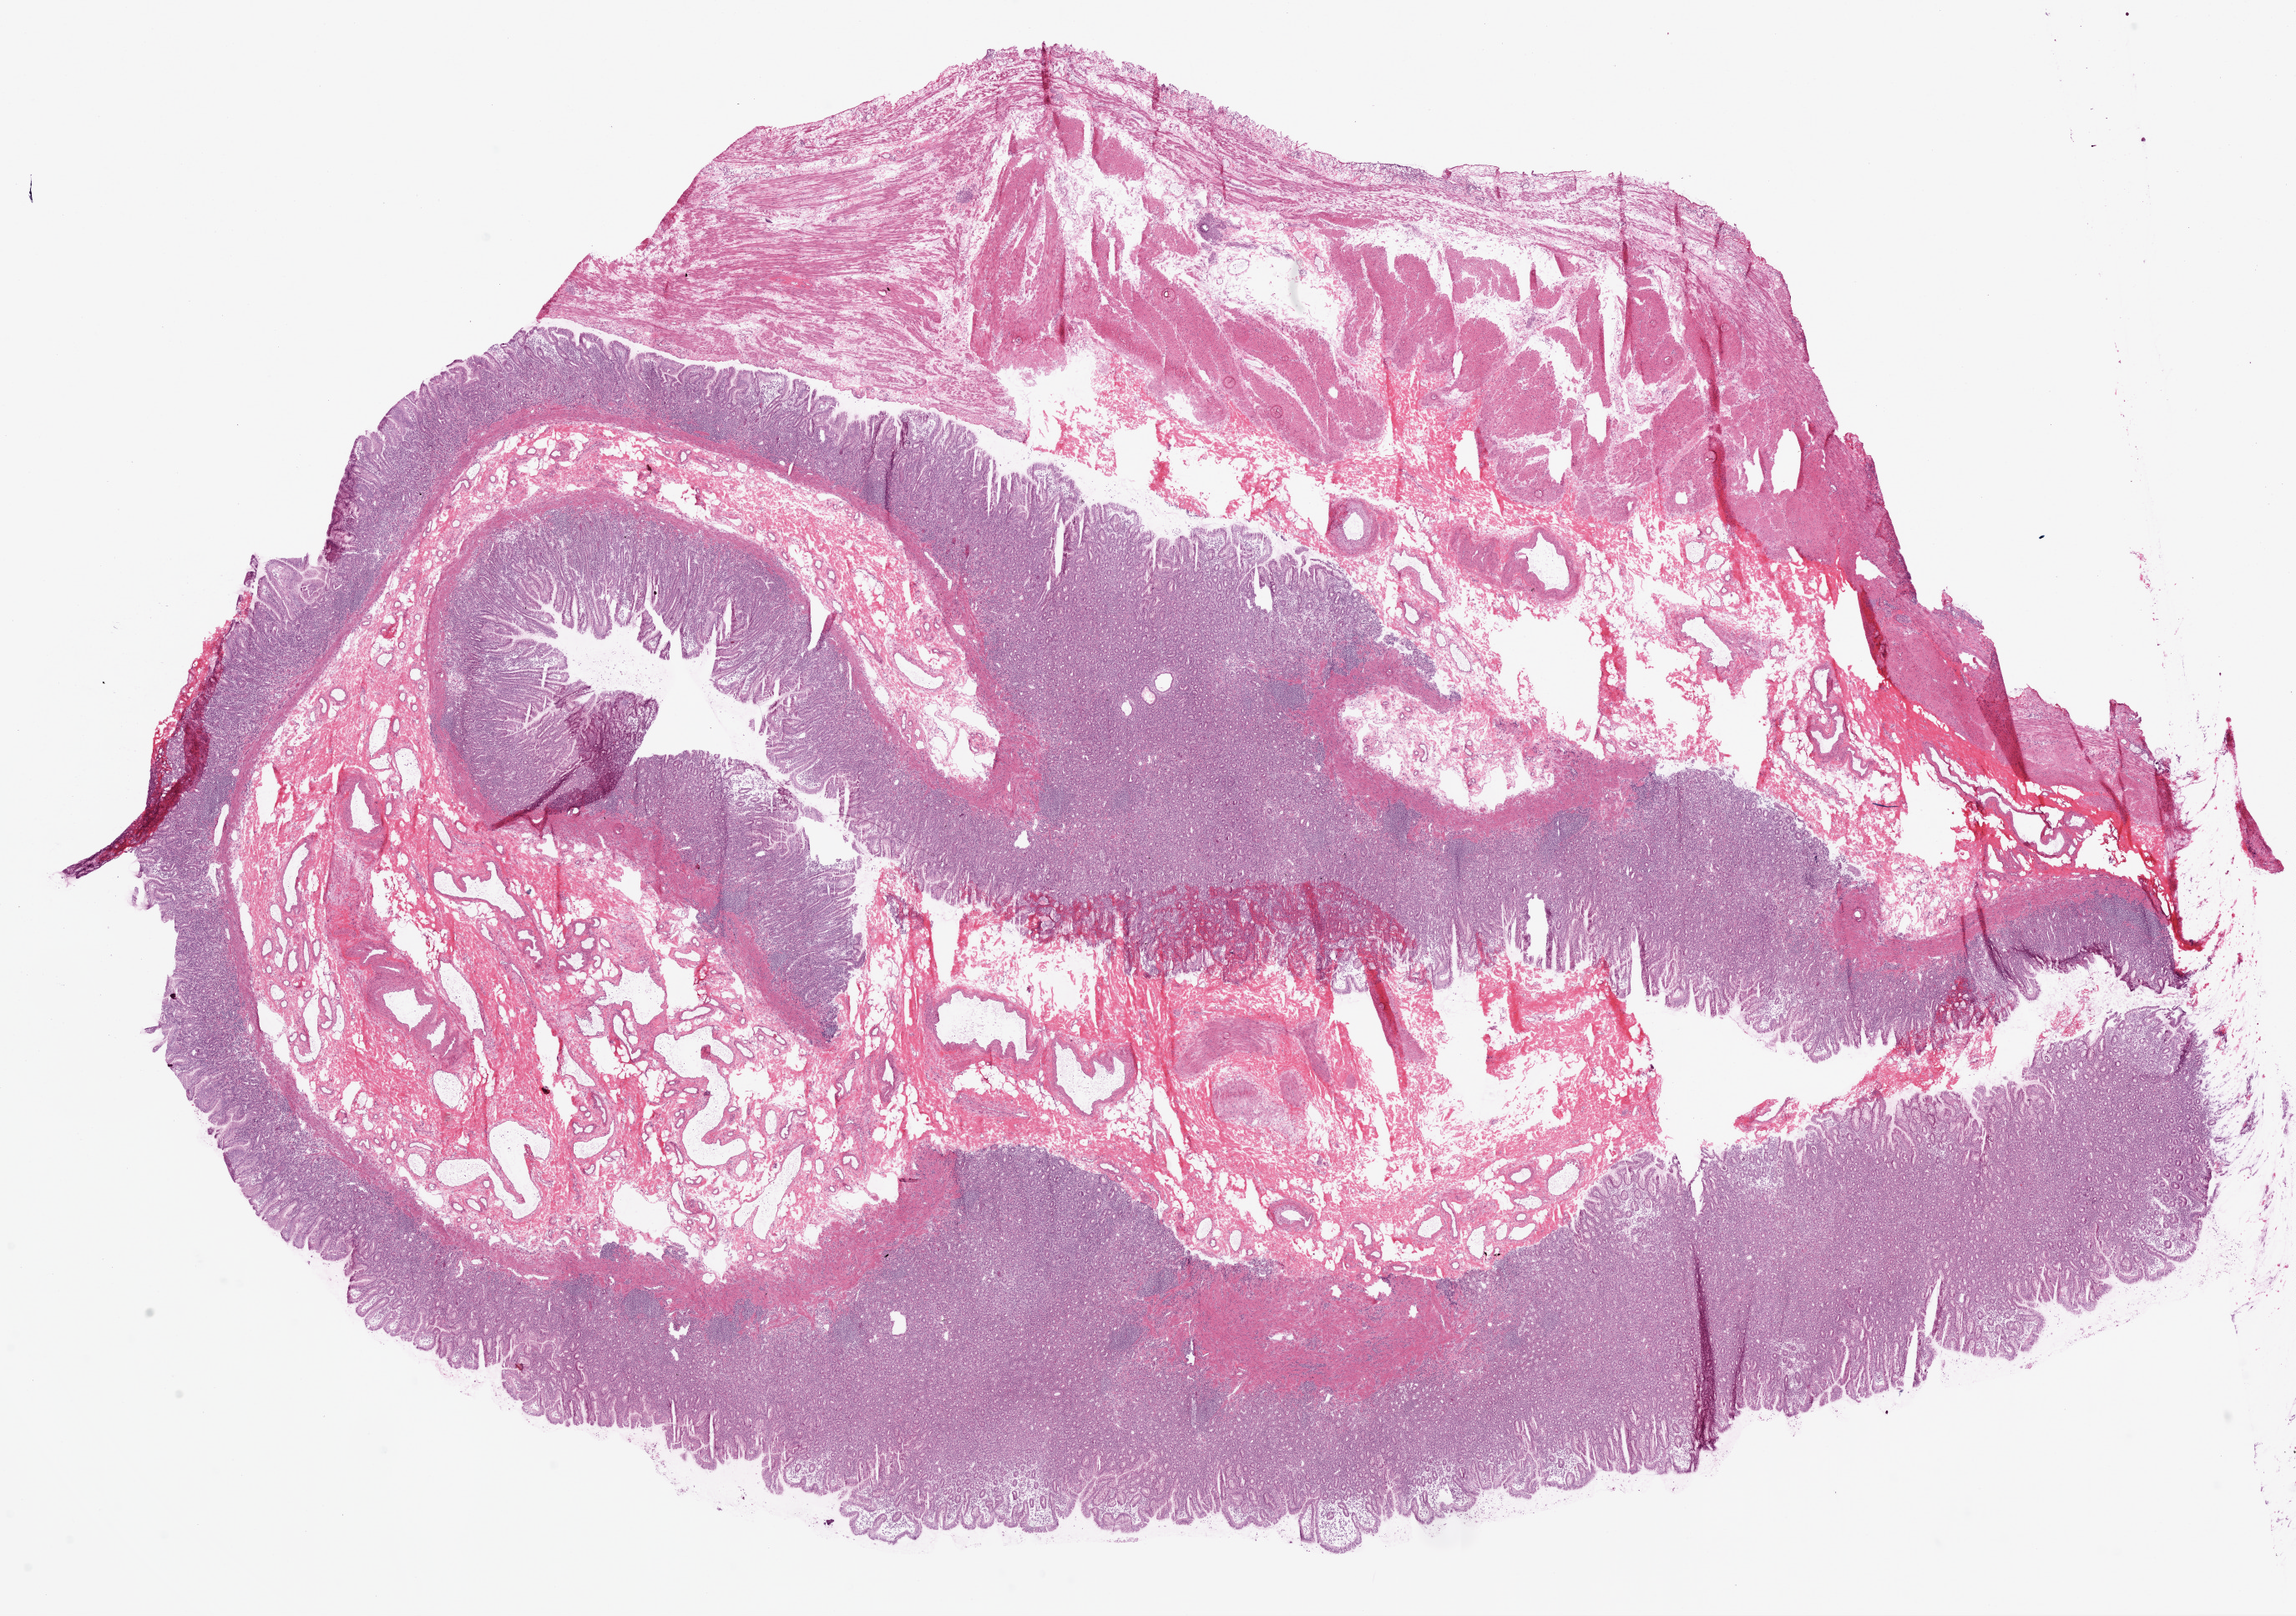
Hematoxylin and eosin (H&E) stained whole-slide image, low-resolution overview of the scanned area, about 22.1 x 15.5 mm (from a 20x scan), frozen section from the top of the tissue portion, solid tissue normal (non-tumour tissue) sample from the stomach. Female patient; age at initial diagnosis 79 years.
This section: solid tissue normal (non-tumour) sample from the same patient. Patient diagnosis: Adenocarcinoma, NOS (gastric antrum).